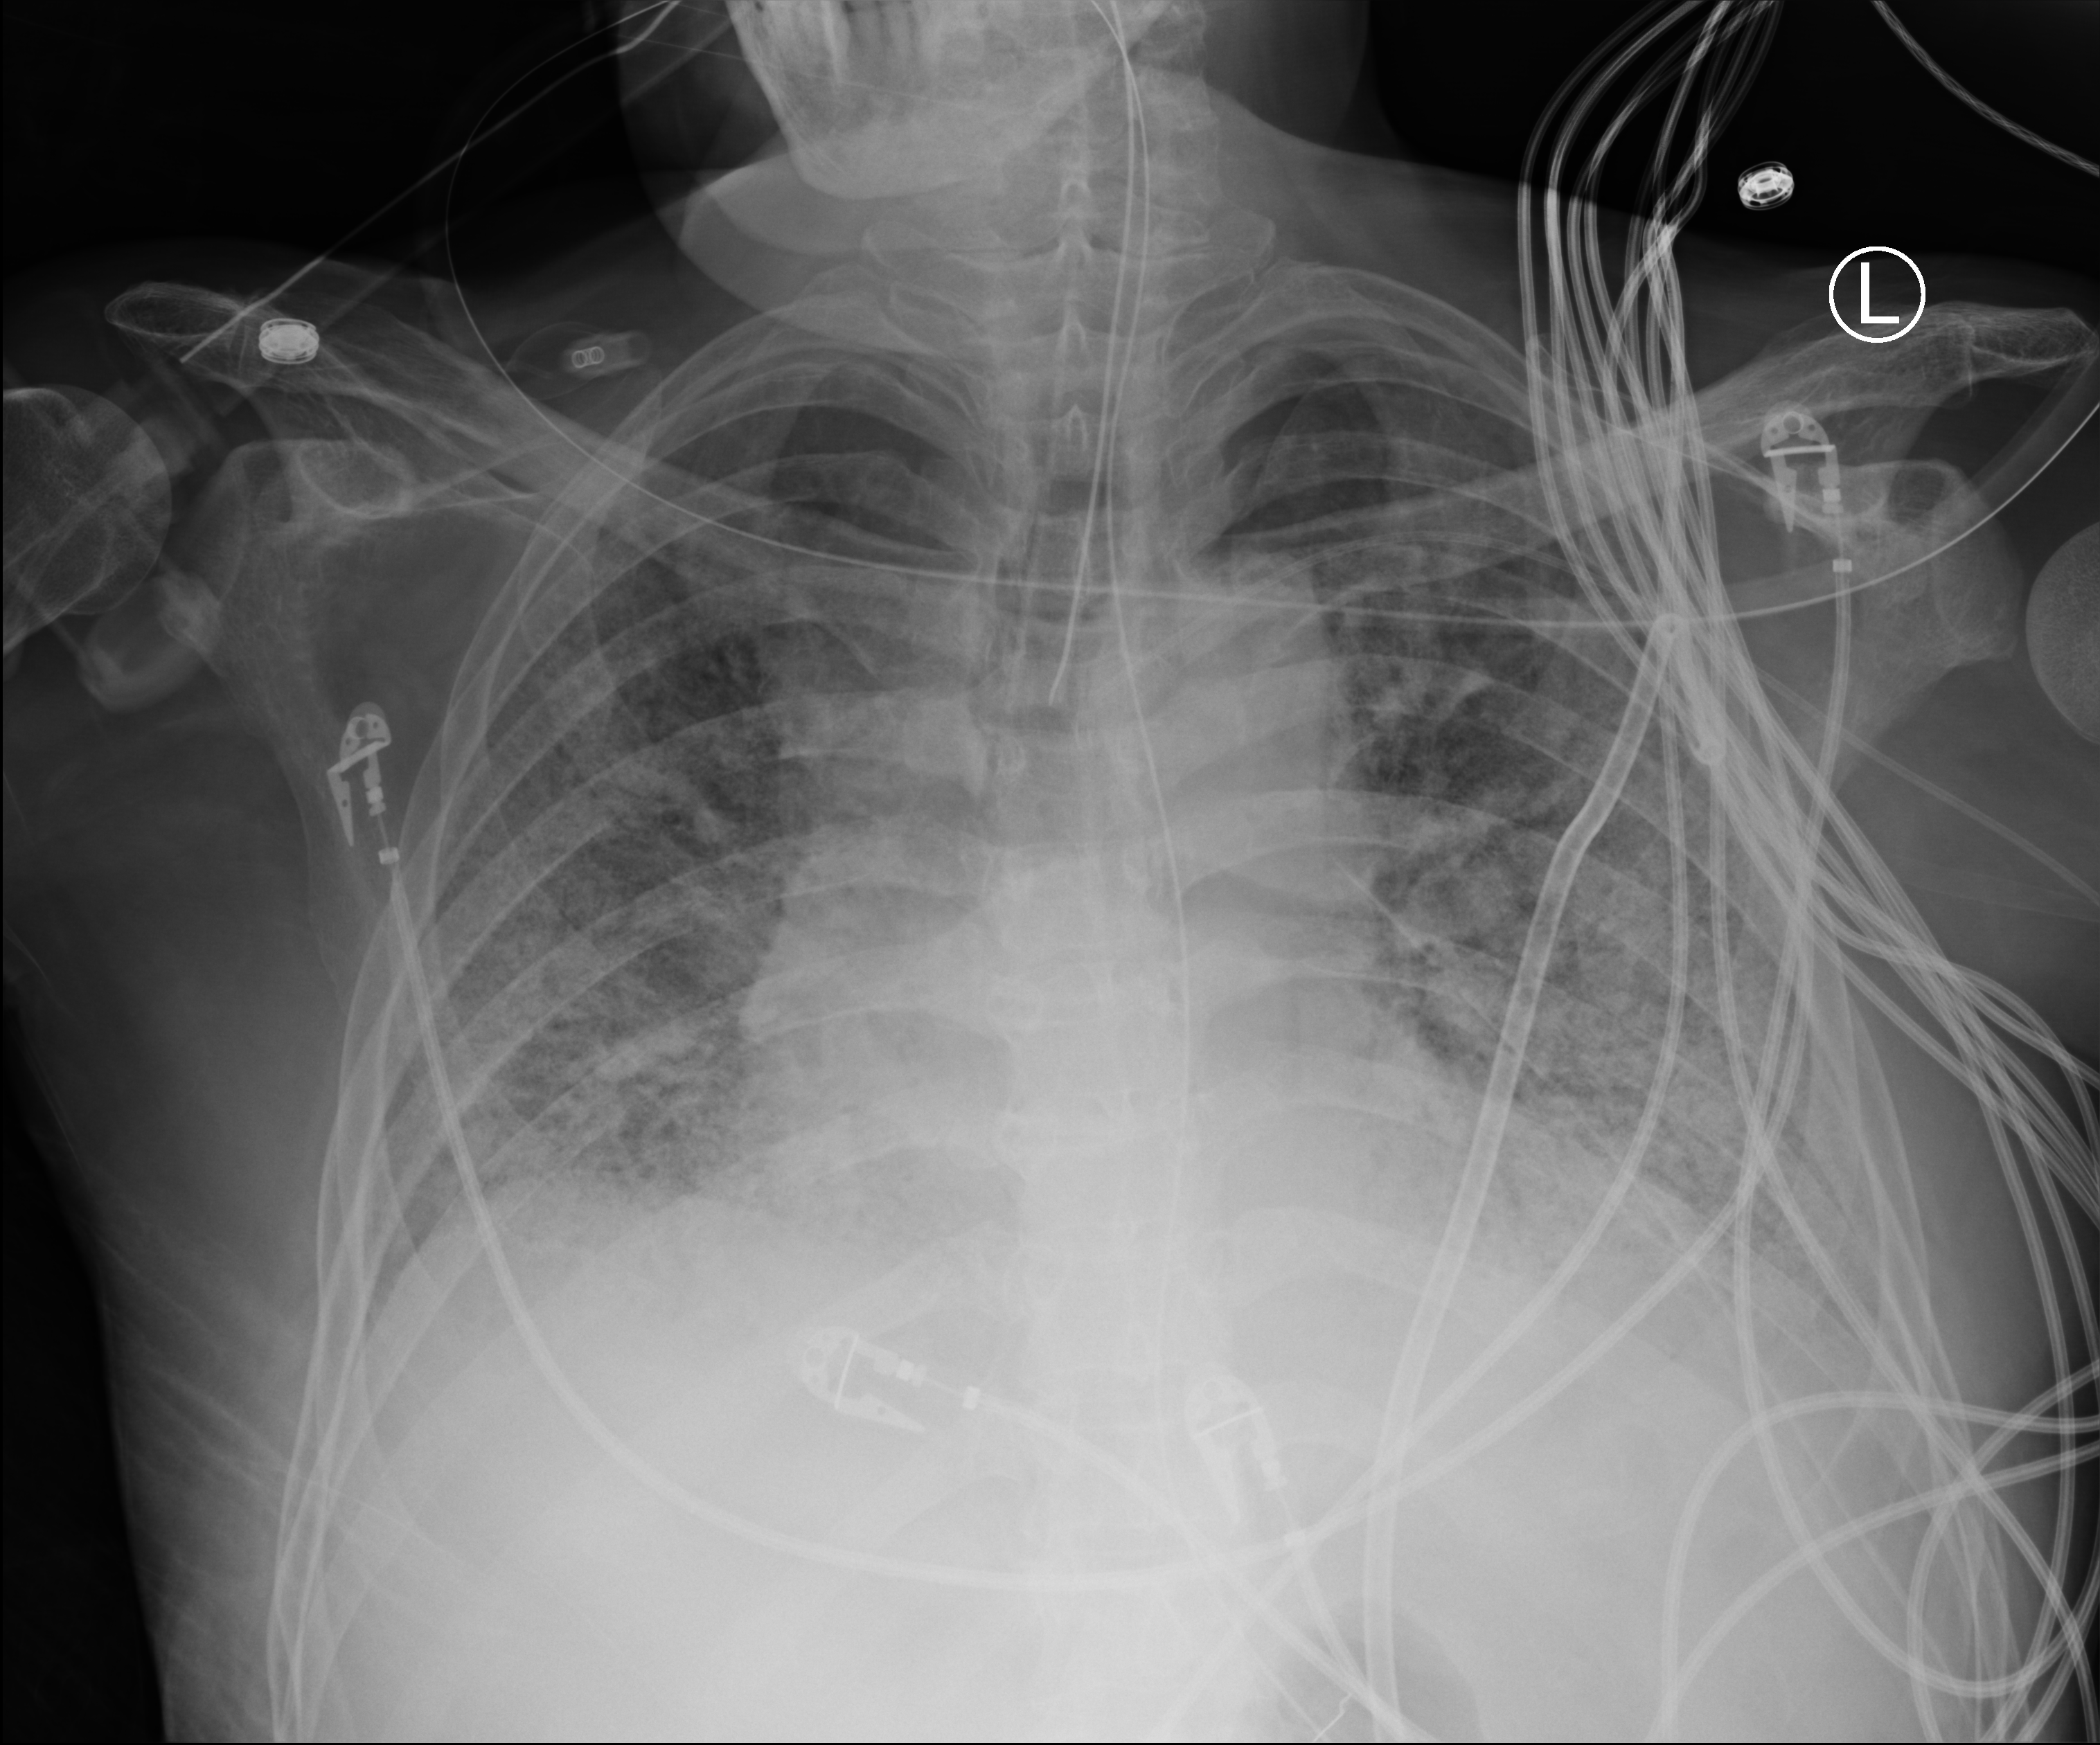
Bedside chest radiograph (computed radiography); anteroposterior (AP) projection. Male patient hospitalised with COVID-19, age 60–74 years.
Admission-level facts for this patient (not findings on this image; timing relative to this image not recorded):
- mechanically ventilated during this hospital stay: yes